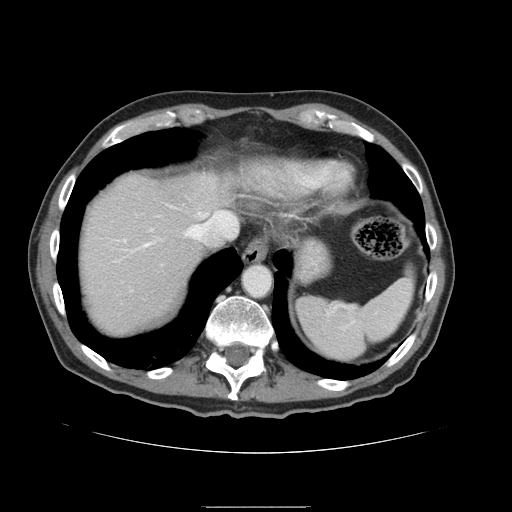
Contrast-enhanced abdominal CT, one axial slice. Slice 129 of 168 in the series (ordered by position). 120 kVp. Intravenous contrast given. Soft-tissue window (W 400 / L 40 HU). 512 × 512 image matrix, field of view 386 × 386 mm. Male patient, age 74 years. Case-level facts recorded for this patient, not image findings: diagnosis: colorectal cancer liver metastases, imaged before liver resection; multiple liver metastases: no; largest metastasis: 14.5 cm.
Structures marked on this image (expert manual segmentation):
- hepatic veins: bounding box [x1, y1, x2, y2] px = [143, 212, 234, 248]
- liver: [78, 170, 237, 337]
- planned liver remnant (the part of the liver to remain after resection): [78, 170, 234, 337]